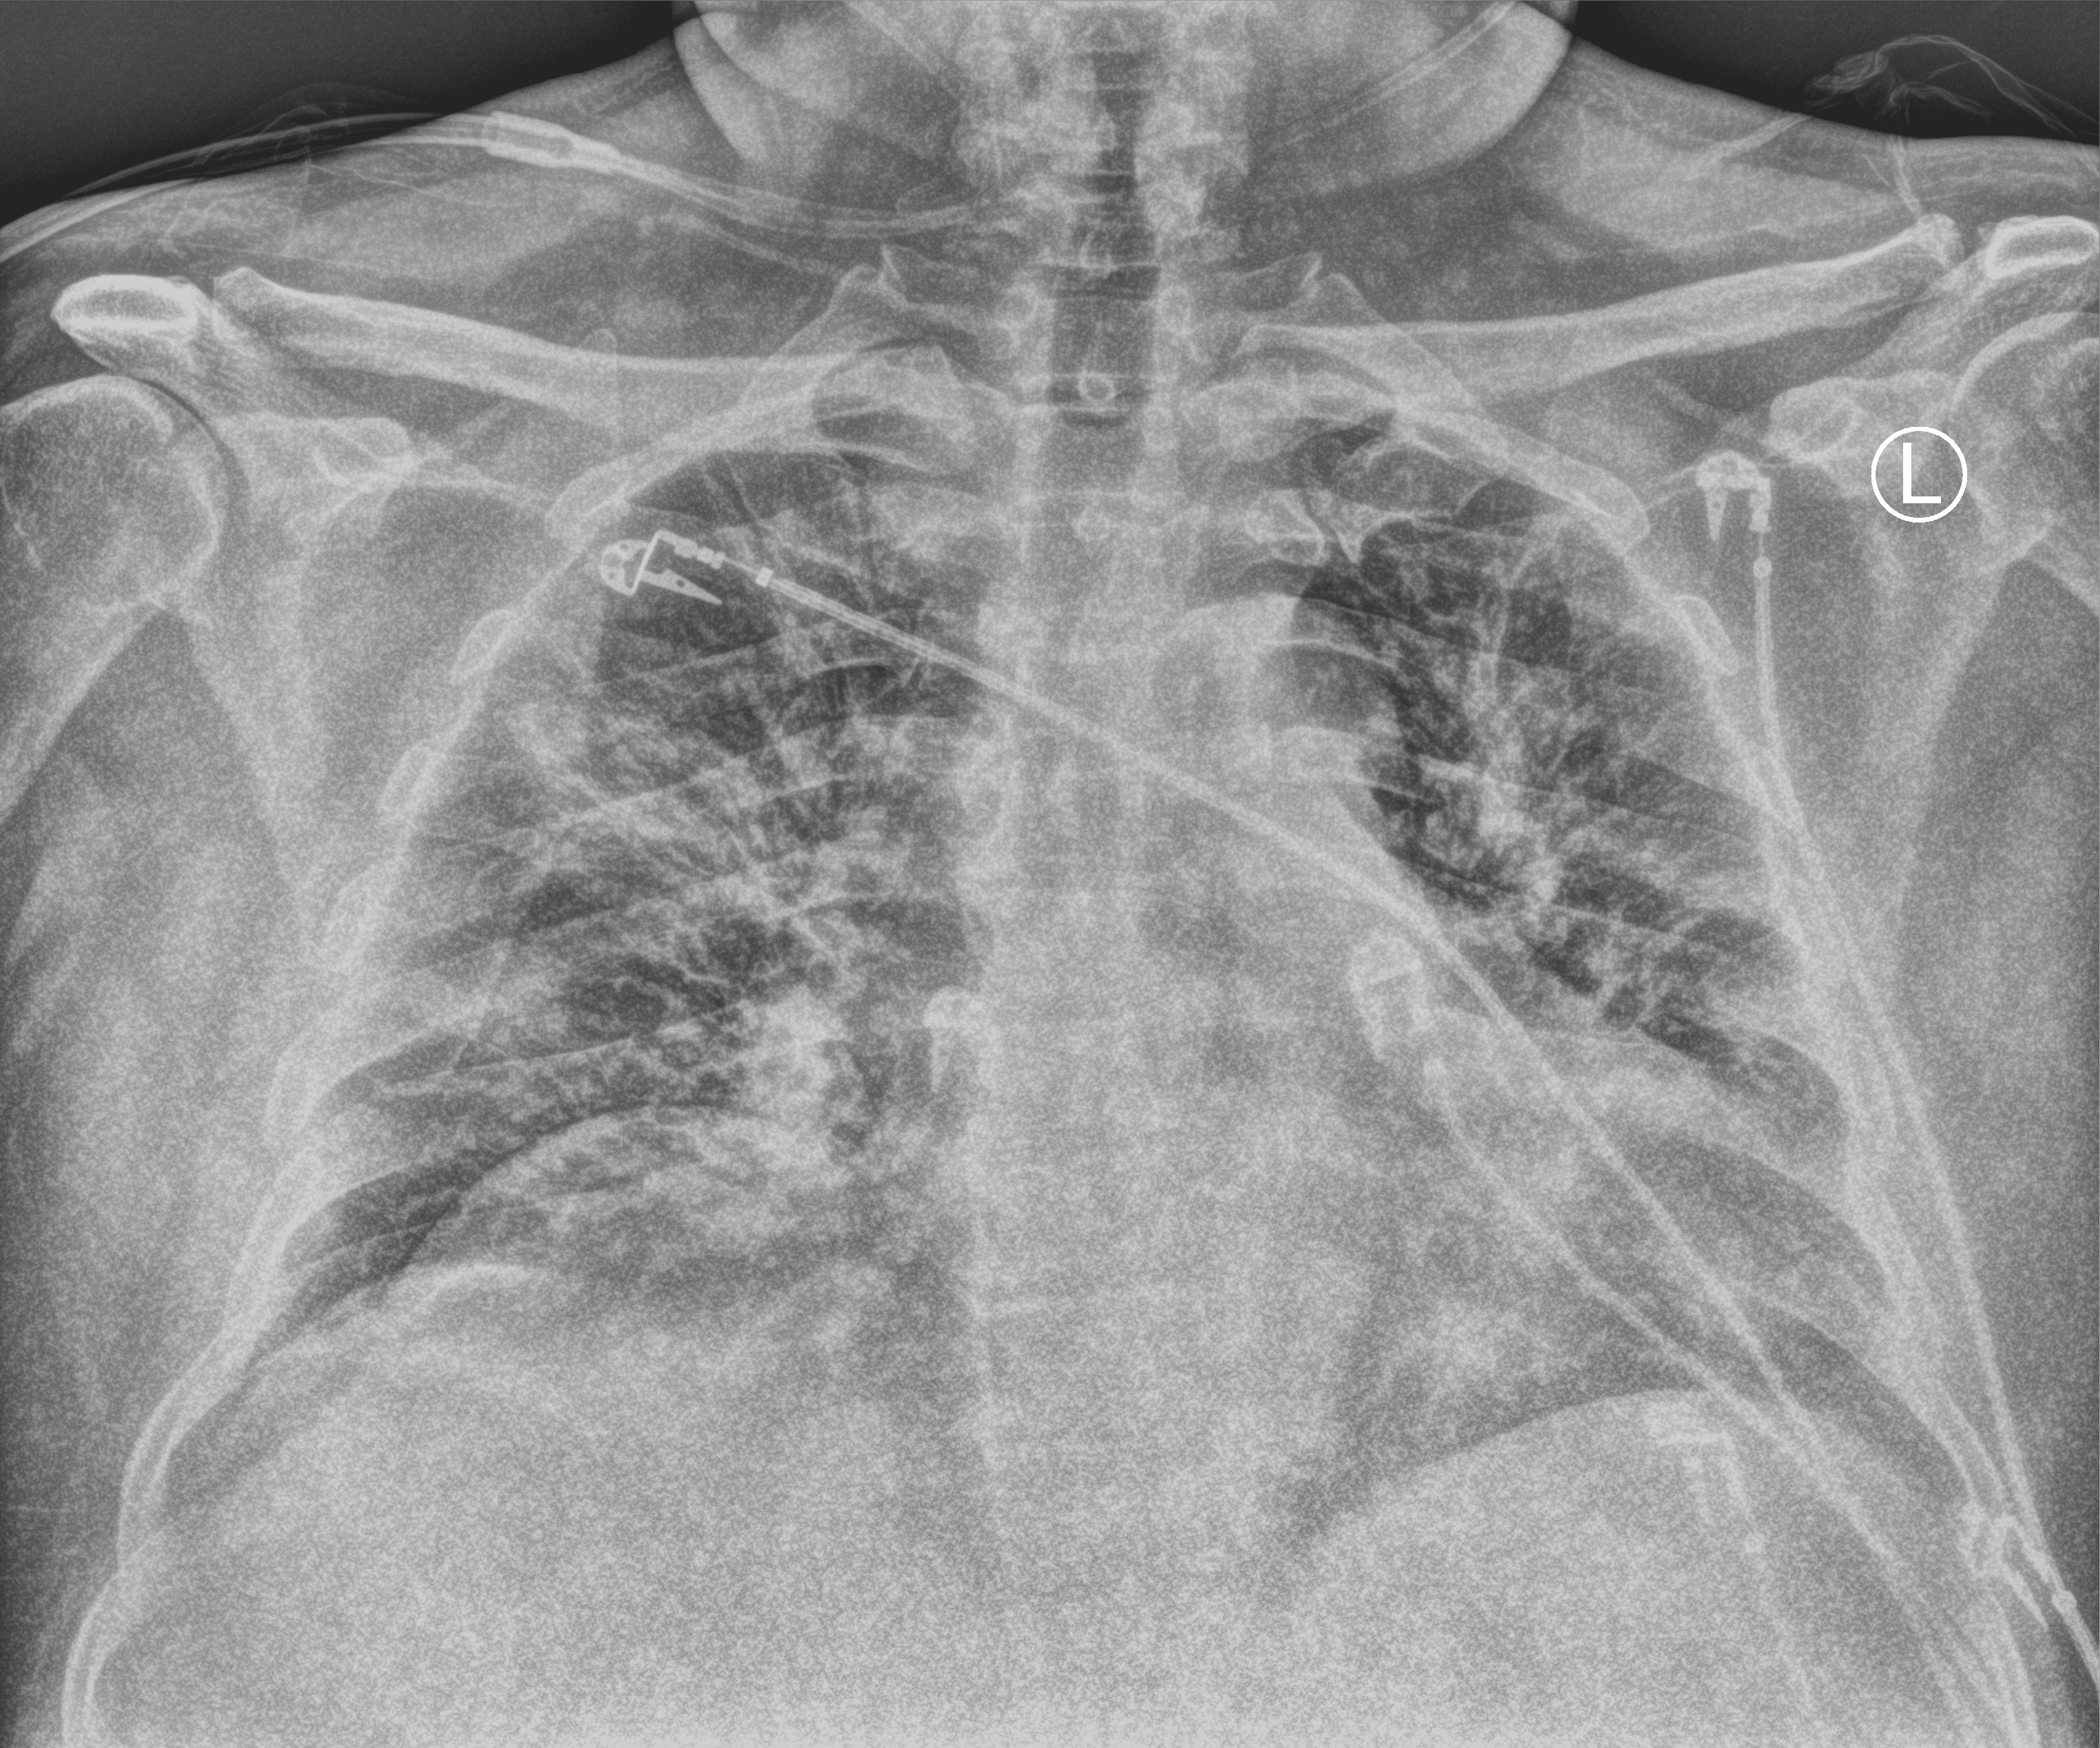
Portable chest radiograph, anteroposterior (AP) projection. Male patient hospitalised with COVID-19, age 60–74 years.
From the hospital-stay record, not from the radiograph (when in the stay this image was taken is not recorded):
- admitted to intensive care during this hospital stay: yes